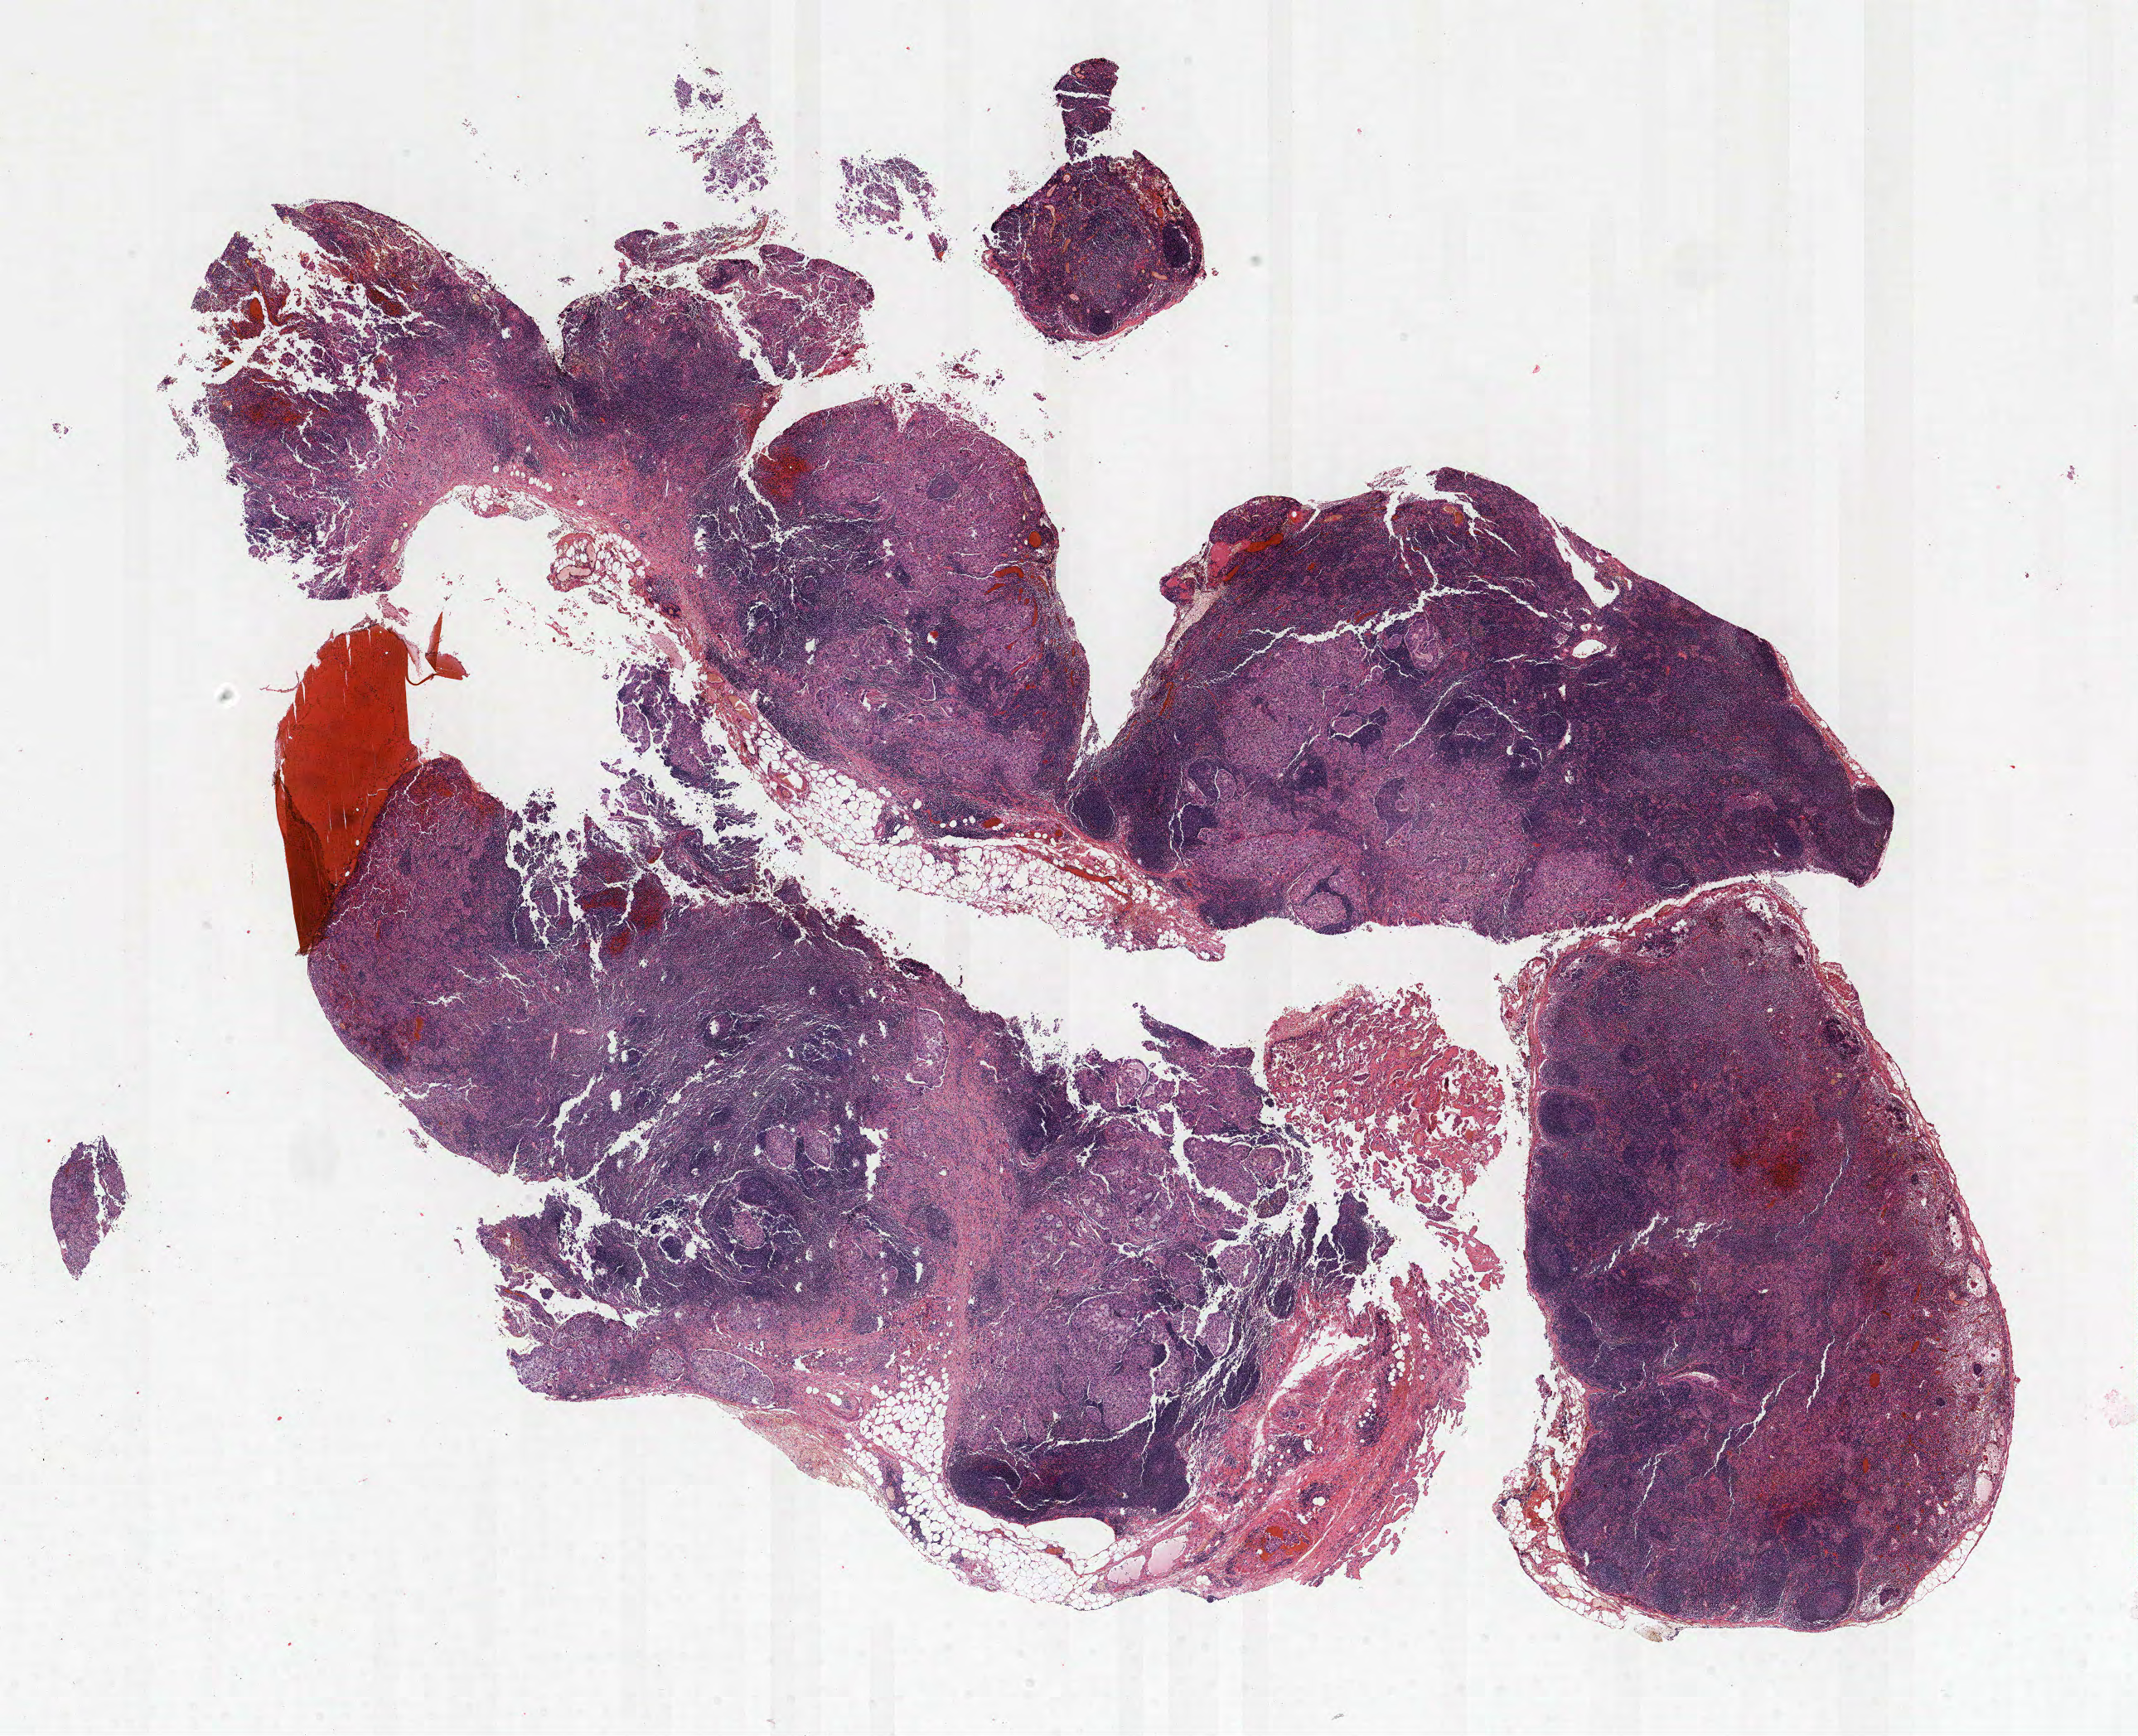
Hematoxylin and eosin (H&E) stained whole-slide image — a low-resolution overview of the entire scanned area, about 20.6 x 16.8 mm. Formalin-fixed paraffin-embedded (FFPE) section. Lung. Male patient, aged 55 at enrolment. Current smoker at enrolment. Grade: moderately differentiated (G2).
Tumour size (pathology): 13 mm. Stage (AJCC 6th edition): IIB. Primary tumour location (clinical record): right upper lobe. Participant's lung-cancer diagnosis: Mucinous adenocarcinoma.